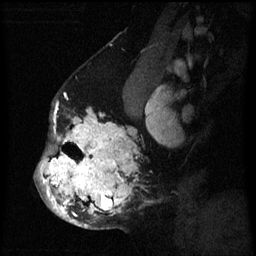
Breast MRI (dynamic contrast-enhanced), one sagittal slice. Slice 39 of 60 in the series (ordered by position). Dynamic contrast-enhanced series, image 2 of 3 at this slice position (ordered by acquisition). 1.5 T. TE 4.2 ms, TR 8 ms. 2 mm slice thickness. 256 × 256 image matrix, field of view 190 × 190 mm. Female patient, age 50 years.
Structures marked on this image (semi-automatic segmentation, software-assisted and operator-edited):
- analysis volume of interest (the breast-tissue region the enhancement analysis was run in; not a lesion): box from (x=34, y=105) to (x=154, y=229) px
- tumour enhancement mask (voxels above the 70 % enhancement threshold inside the analysis volume of interest): (x=40, y=108)–(x=136, y=227)